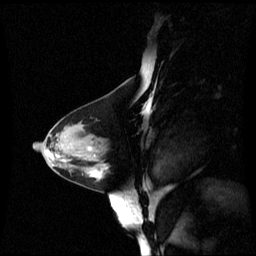
Breast MRI (dynamic contrast-enhanced), one sagittal slice. Dynamic contrast-enhanced series, image 2 of 3 at this slice position (ordered by acquisition). 1.5 T. TE 4.2 ms, TR 8.4 ms. 2.4 mm slice thickness. 256 × 256 image matrix, field of view 250 × 250 mm. Patient: female, 44 years. Case-level facts recorded for this patient, not image findings: setting: breast cancer imaged before/during neoadjuvant chemotherapy; receptor status: triple-negative.
Structures marked on this image (semi-automatically segmented with operator editing):
- analysis volume of interest (the breast-tissue region the enhancement analysis was run in; not a lesion): bounding box <79,148,109,188> (left, top, right, bottom; pixels)
- tumour enhancement mask (voxels above the 70 % enhancement threshold inside the analysis volume of interest): <94,169,108,177>